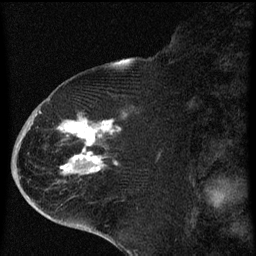
Breast MRI (dynamic contrast-enhanced), one sagittal slice. Slice 27 of 60 in the series (ordered by position). Dynamic contrast-enhanced series, image 2 of 4 at this slice position (ordered by acquisition). 1.5 T. TE 4.2 ms, TR 8 ms. 256 × 256 image matrix, field of view 180 × 180 mm. Female patient, age 71 years.
Annotated regions visible in this slice (semi-automatically segmented with operator editing):
- analysis volume of interest (the breast-tissue region the enhancement analysis was run in; not a lesion): bounding box [x1, y1, x2, y2] px = [32, 86, 139, 205]
- tumour enhancement mask (voxels above the 70 % enhancement threshold inside the analysis volume of interest): [39, 112, 127, 175]